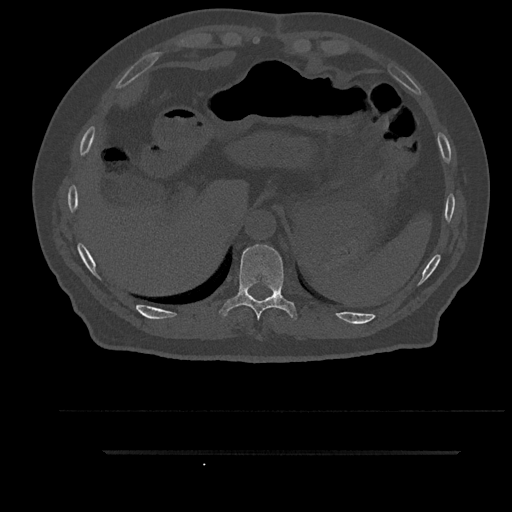
CT including the spine, one axial slice. Reconstruction kernel Br40s/3. Bone window (W 1800 / L 400 HU). 0.5 mm slice thickness. 512 × 512 image matrix. Male patient, age 63 years. From the clinical record (not read from this slice): primary cancer: renal; vertebrae with lytic lesions (as recorded): T8.
Structures marked on this image (semi-automatic segmentation, software-assisted and operator-edited):
- T10 vertebra: bounding box (x1, y1, x2, y2) in pixels: (219, 244, 298, 319)